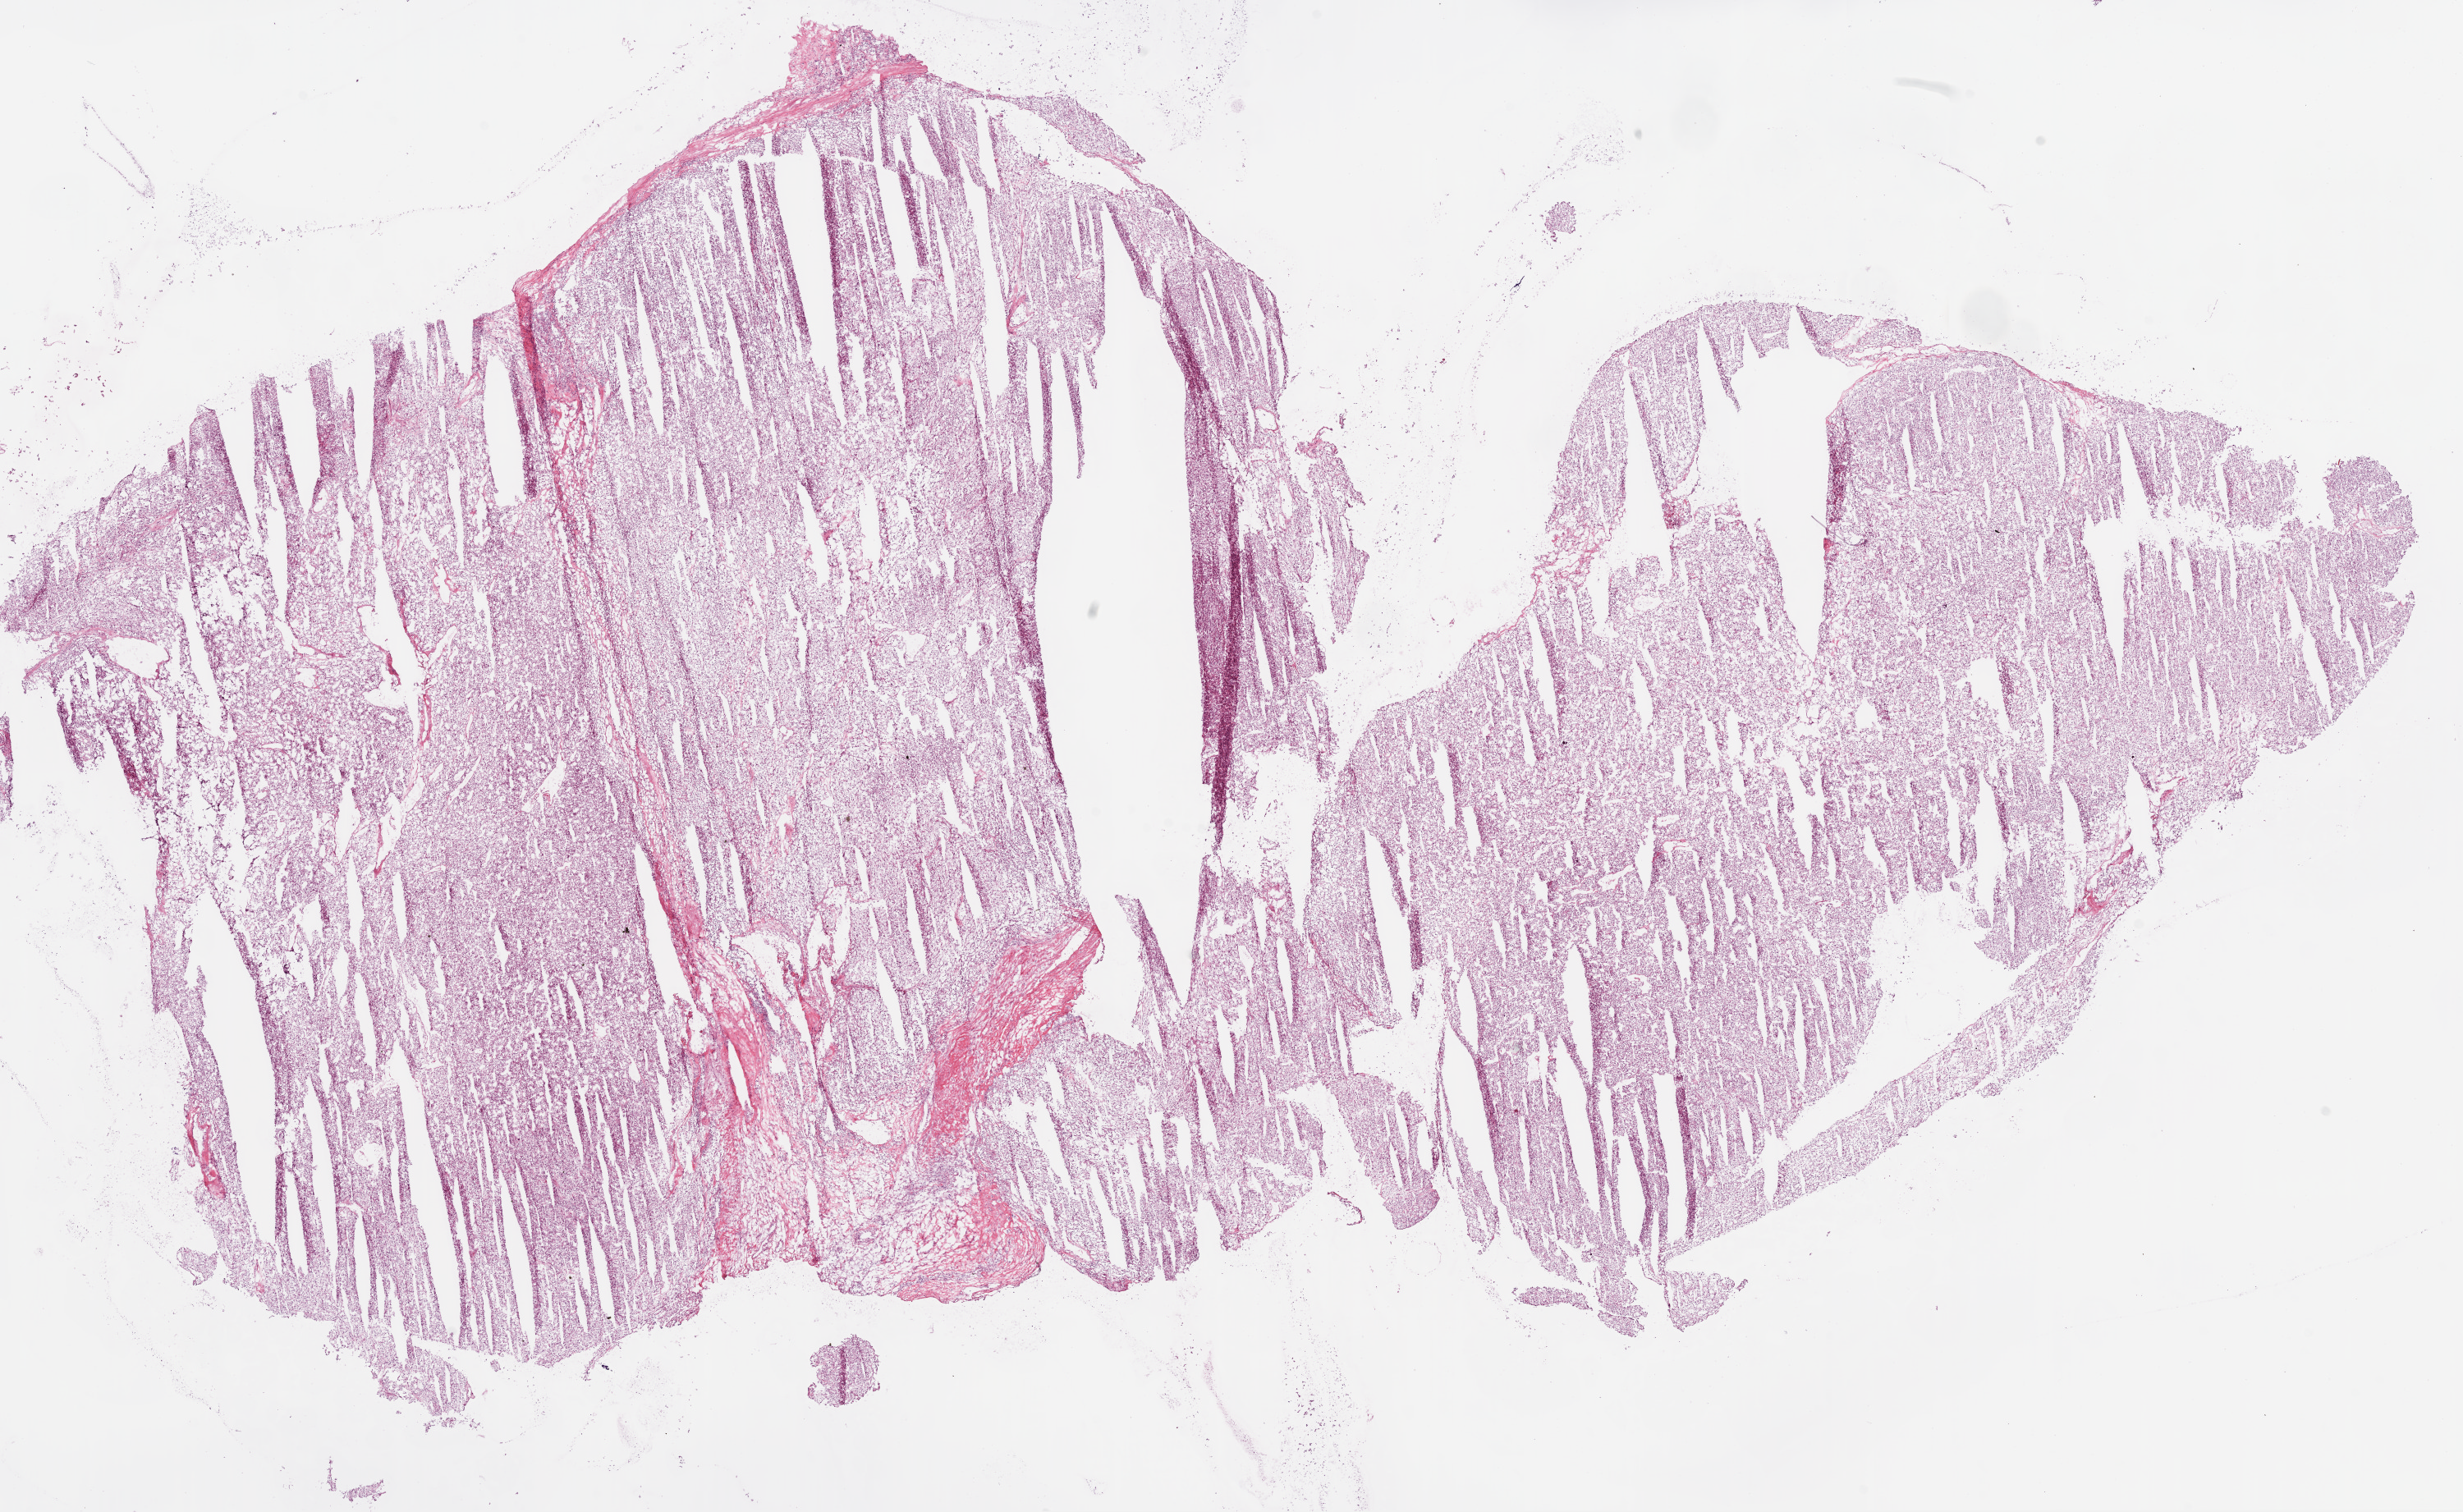
H&E whole-slide image — low-resolution overview of the scanned area, about 24.1 x 14.8 mm (slide scanned at 20x), frozen section from the bottom of the tissue portion, primary tumour sample from the kidney. Patient: female, age at initial diagnosis 88 years.
Histologic diagnosis: Clear cell adenocarcinoma, NOS.